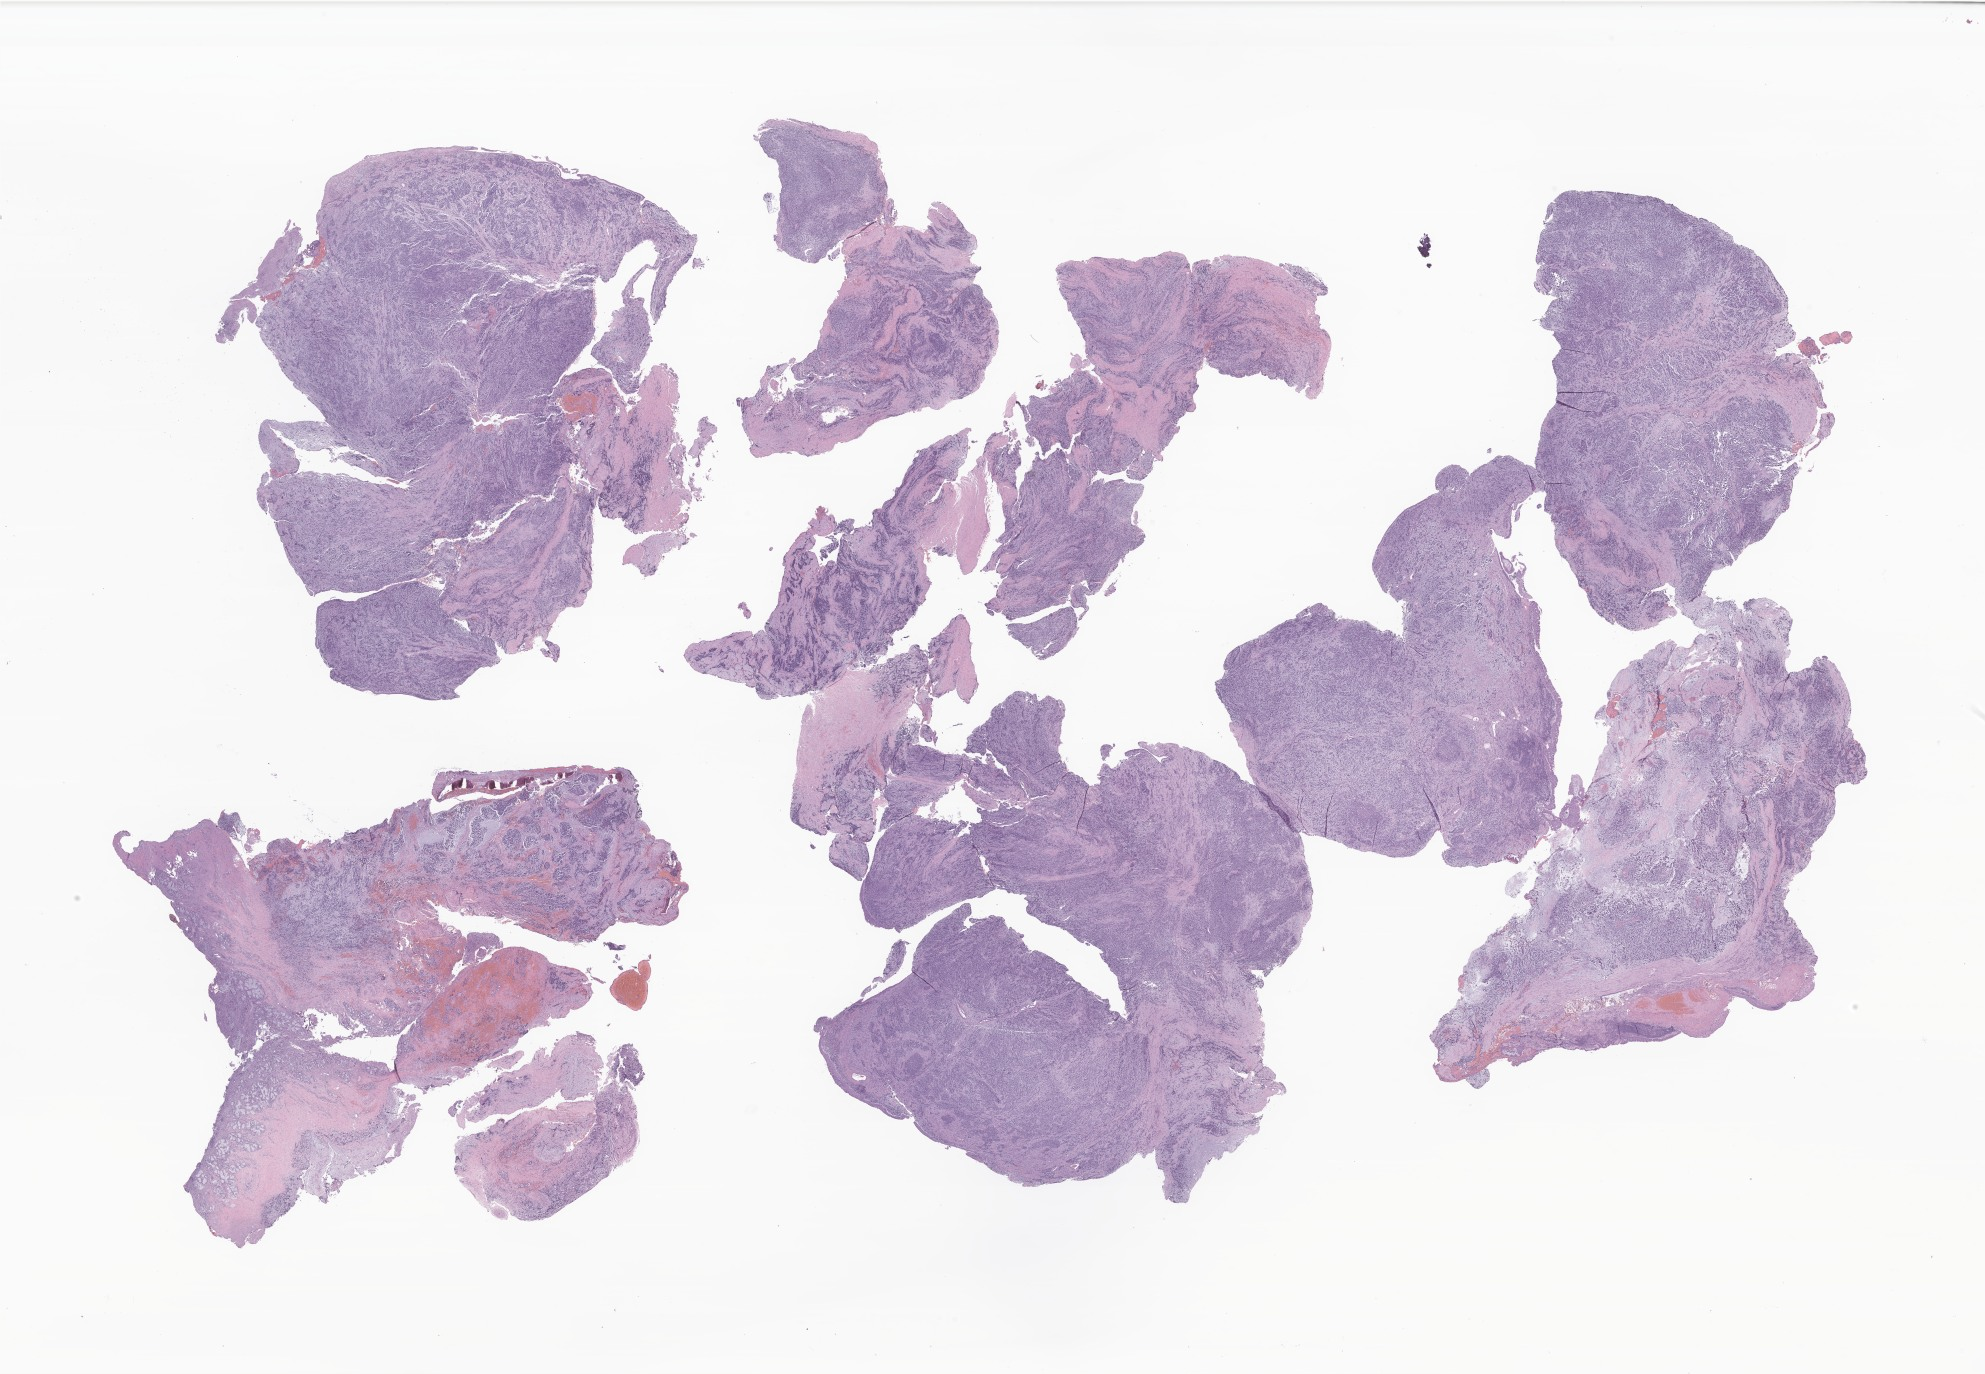
H&E whole-slide image of tumor tissue from the nasopharynx — shown as a low-resolution overview of the whole scanned area (about 33.5 x 23.2 mm), formalin-fixed paraffin-embedded section. Patient: female, age 49 months (4 years 1 month).
Diagnosis (ICD-O-3 morphology term): Embryonal rhabdomyosarcoma, NOS.